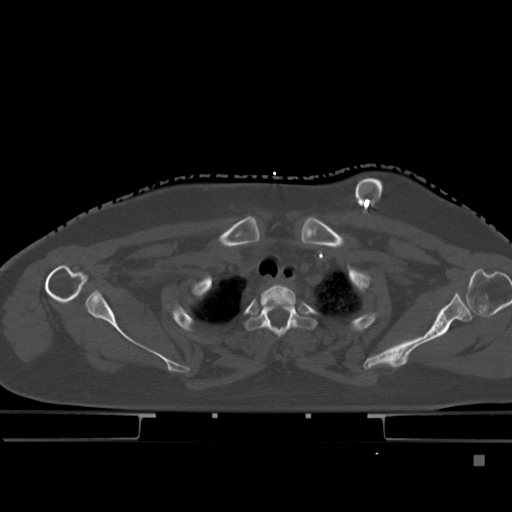
CT including the spine, one axial slice. Slice 362 of 495 in the series (ordered by position). Bone window (W 1800 / L 400 HU). 1.5 mm slice thickness. 512 × 512 image matrix. Female patient, age 33 years. From the clinical record (not read from this slice): primary cancer: breast.
Annotated regions visible in this slice (semi-automatic segmentation, software-assisted and operator-edited):
- T1 vertebra: box from (x=261, y=284) to (x=296, y=321) px
- T2 vertebra: (x=246, y=304)–(x=316, y=338)